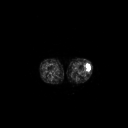
FDG PET of an extremity soft-tissue mass (from a PET/CT study), one axial slice. Slice 177 of 223 in the series (ordered by position). 128 × 128 image matrix, field of view 700 × 700 mm. Patient: female, 16 years. From the clinical record (not read from this slice): histological type: spindle cell suggestive of biphasic synovial sarcoma; grade: intermediate; site of the primary tumour: left knee.
Outlined on this slice (expert contour drawn on MRI and transferred to this co-registered scan by the dataset authors):
- gross tumour volume including surrounding oedema: bounding box [x1, y1, x2, y2] px = [85, 62, 91, 71]
- gross tumour volume (mass): [85, 62, 91, 71]